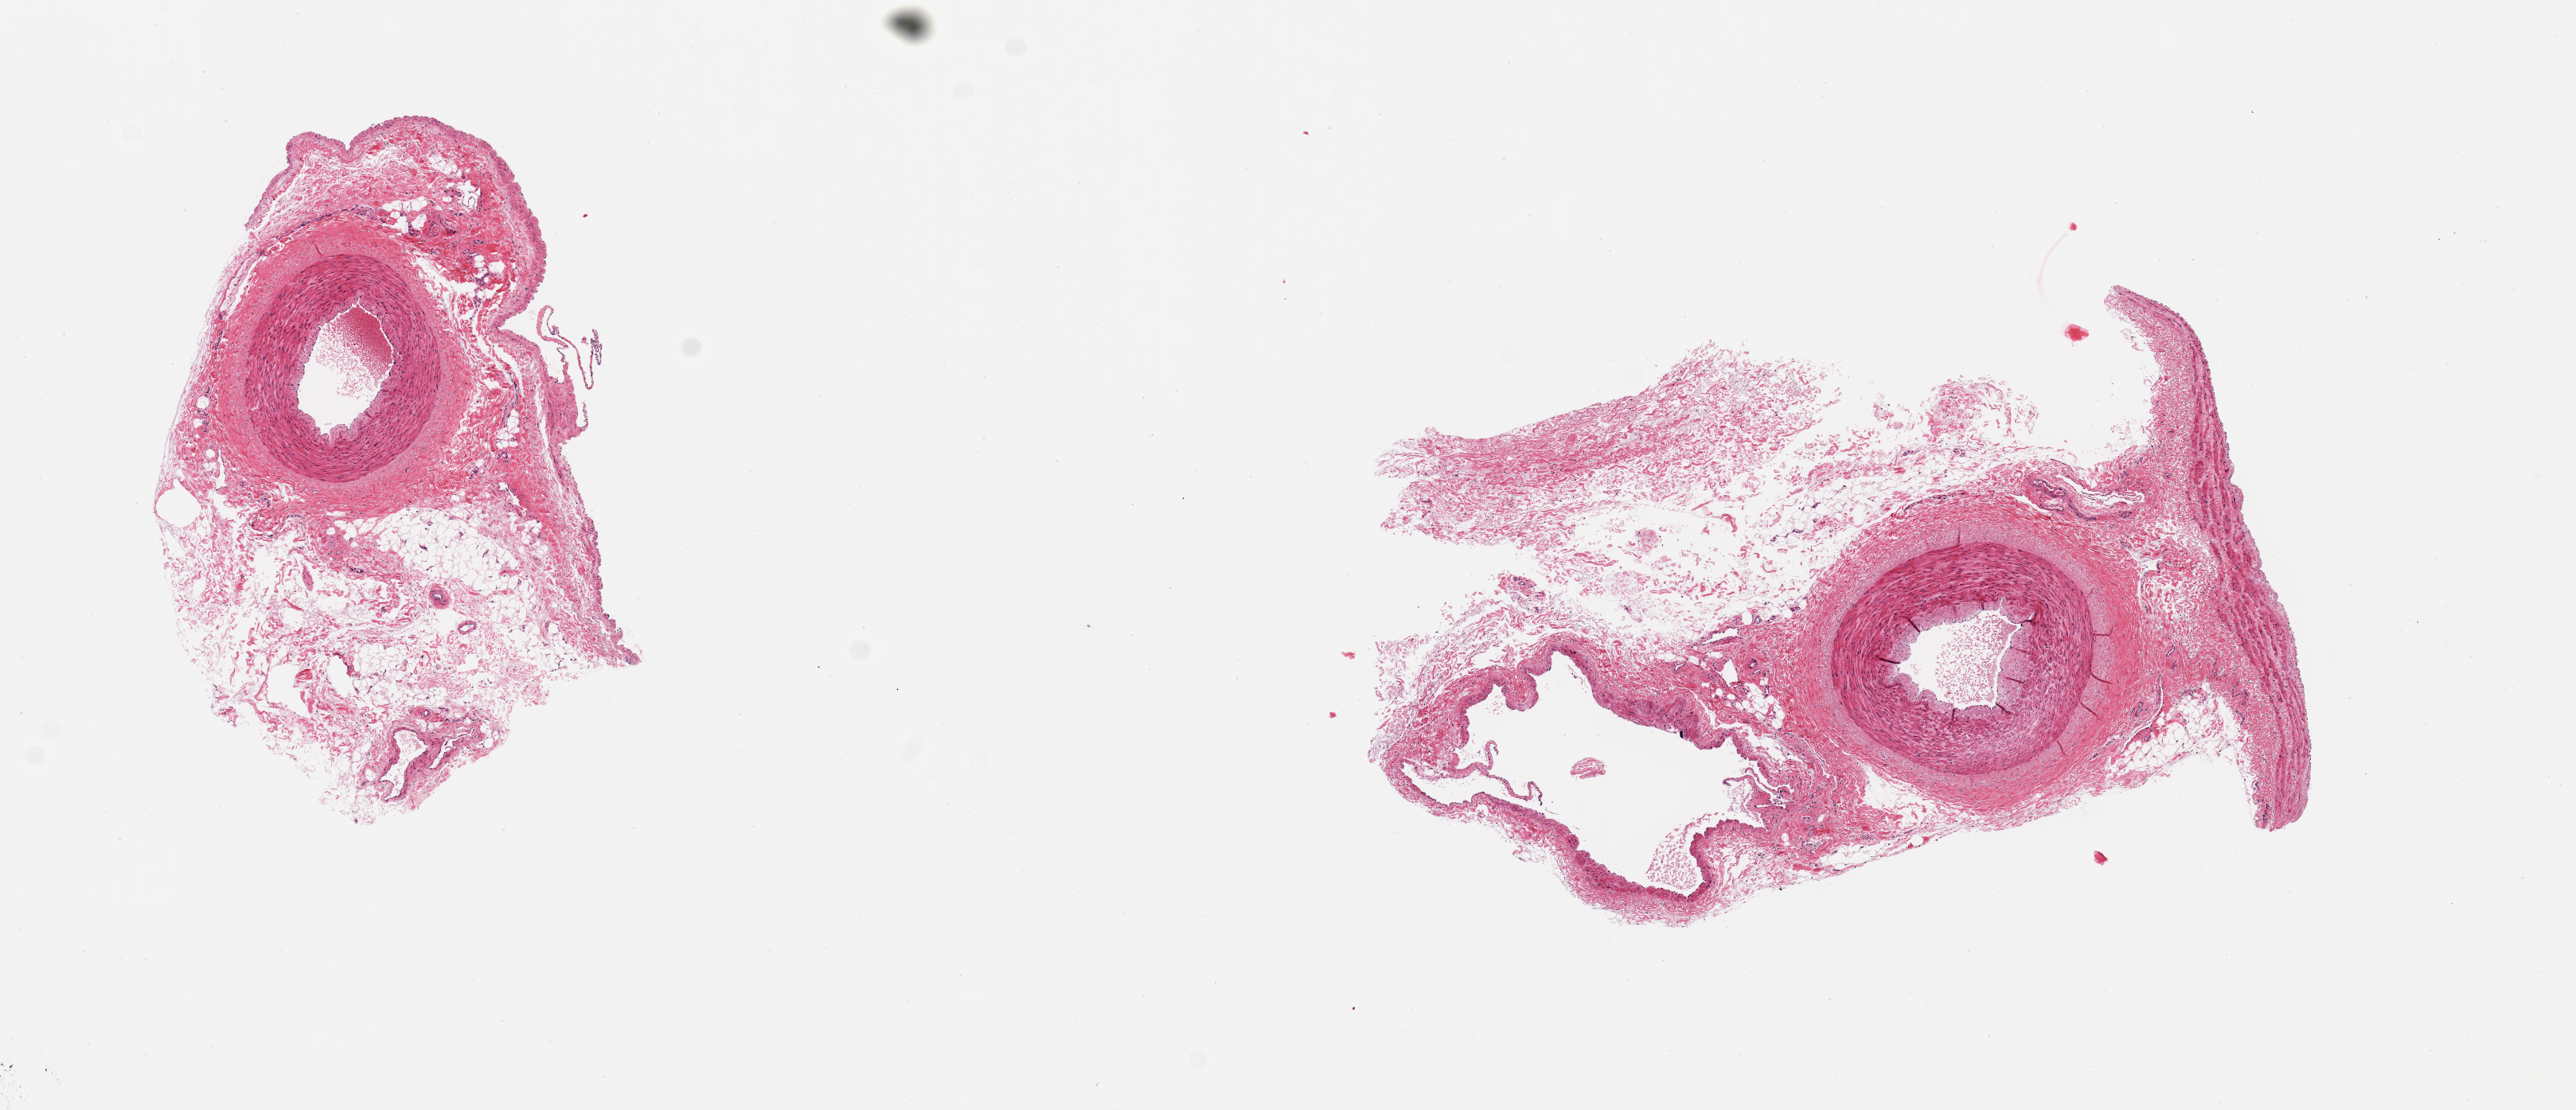
Hematoxylin and eosin (H&E) whole-slide image, low-resolution overview of the scanned area, about 12.8 x 5.5 mm (from a 20x scan). PAXgene-fixed, paraffin-embedded tissue. Sampled site (target tissue): tibial artery. Donor tissue sample. Donor: female.
Review note (as recorded): 2 pieces, 1 with 1 mm artery and vein; 1 with 1 mm artery; each with 20% fat and stroma.